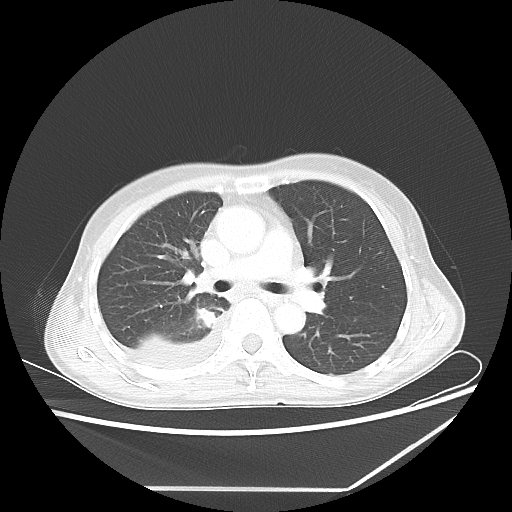
Chest CT, one axial slice. Position 37 of 60 along the scan axis. Reconstruction kernel LUNG. 80 kVp. Lung window (W 1500 / L -600 HU). 5 mm slice thickness. 512 × 512 image matrix, field of view 364 × 364 mm. Female patient, age 59 years. Case-level facts recorded for this patient, not image findings: clinical TNM (as recorded): T1c N1 M1.
Annotated regions visible in this slice (bounding box drawn by a radiologist):
- lung tumour (recorded histology: adenocarcinoma): bounding box (x1, y1, x2, y2) in pixels: (193, 303, 218, 330)